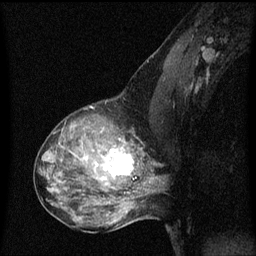
Breast MRI (dynamic contrast-enhanced), one sagittal slice. Position 36 of 60 along the scan axis. Dynamic contrast-enhanced series, image 2 of 3 at this slice position (ordered by acquisition). 1.5 T. TE 4.2 ms, TR 8 ms. 2 mm slice thickness. 256 × 256 image matrix, field of view 200 × 200 mm. Female patient, age 50 years.
Structures marked on this image (semi-automatically segmented with operator editing):
- analysis volume of interest (the breast-tissue region the enhancement analysis was run in; not a lesion): bounding box <91,126,141,189> (left, top, right, bottom; pixels)
- tumour enhancement mask (voxels above the 70 % enhancement threshold inside the analysis volume of interest): <96,142,134,179>